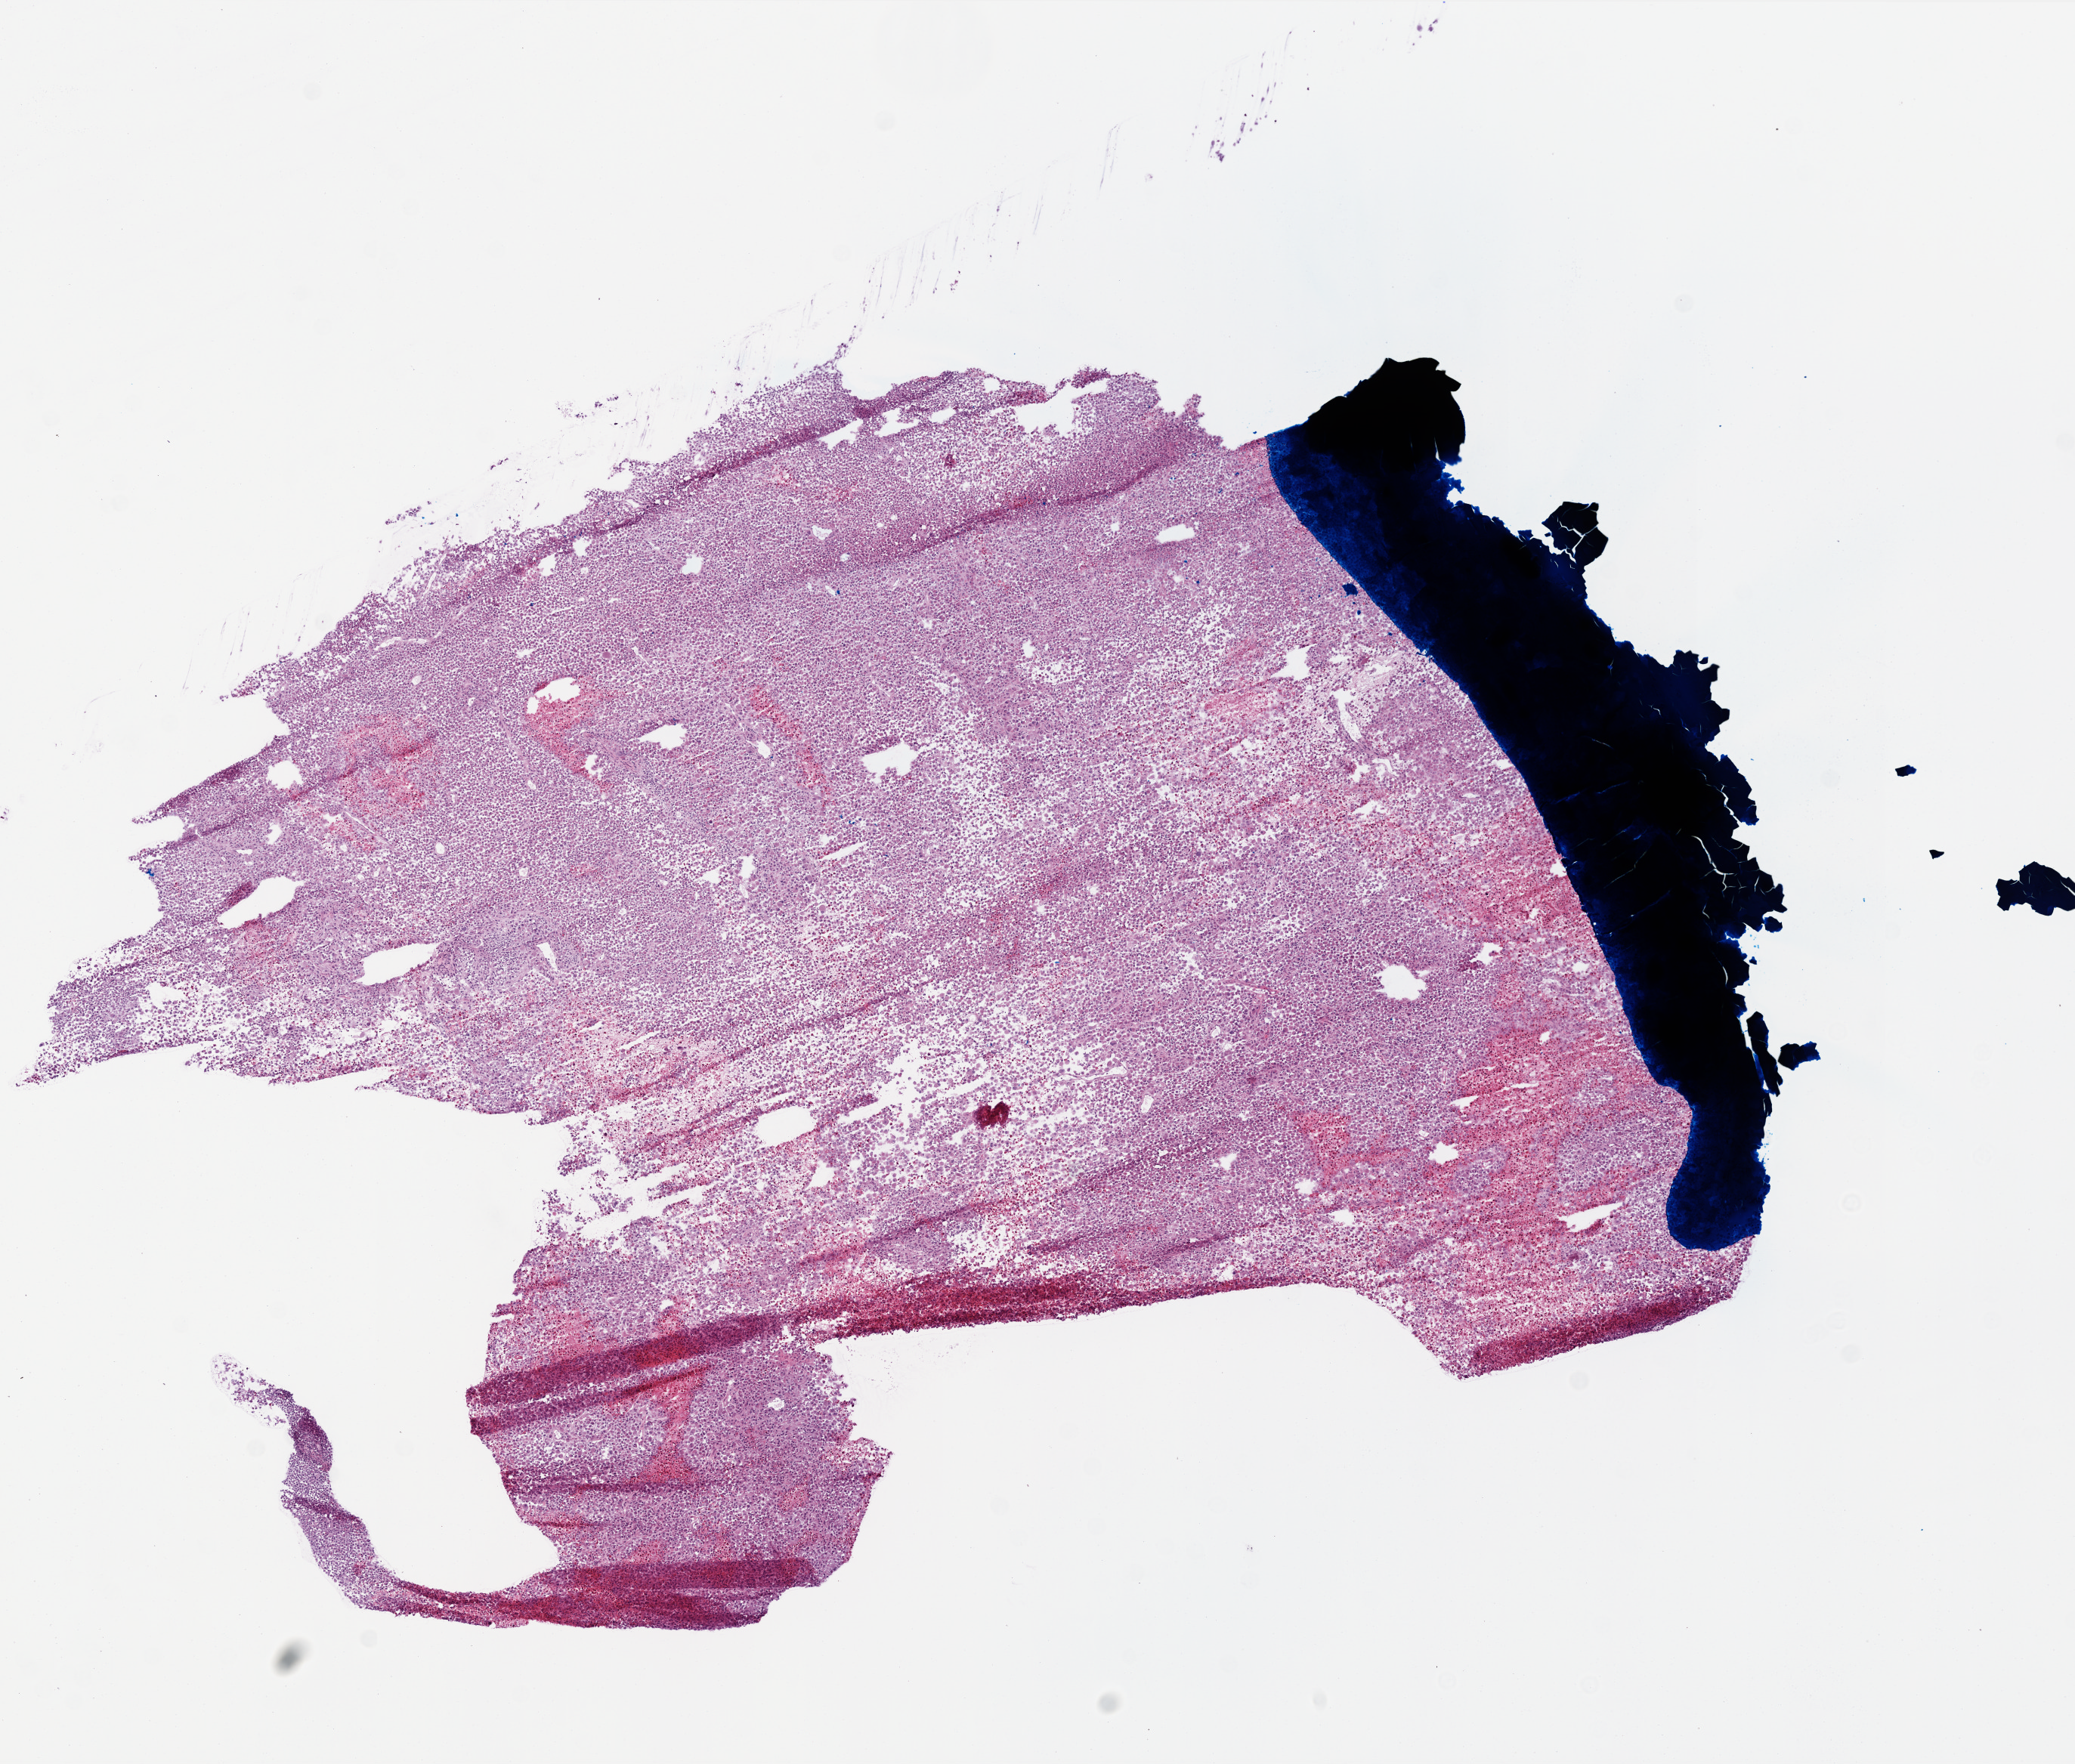
Digitized Hematoxylin and eosin (H&E) stained tissue section (whole slide), whole scanned area (about 11.0 x 9.3 mm, acquisition: 20x scan) shown as a low-resolution overview. Frozen section. Primary tumour sample from the brain. Patient: male, age at initial diagnosis 60 years. Composition of this section per pathologist review: tumour cells 90%, tumour nuclei 100%, normal cells 0%, stromal cells 0%, necrosis 10%.
- histologic diagnosis: Glioblastoma